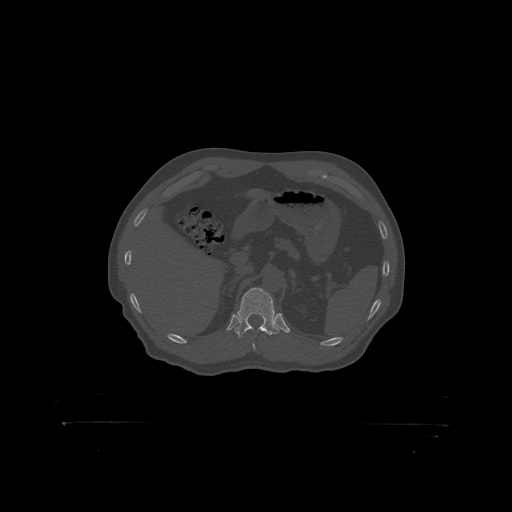
CT including the spine, one axial slice; position 357 of 399 along the scan axis; reconstruction kernel STANDARD; 120 kVp; bone window (W 1800 / L 400 HU); 512 × 512 image matrix, field of view 650 × 650 mm. Patient: male, 46 years. Case-level facts recorded for this patient, not image findings: primary cancer: skin.
Annotated regions visible in this slice (semi-automatic segmentation, software-assisted and operator-edited):
- T12 vertebra: bounding box <237,288,280,319> (left, top, right, bottom; pixels)